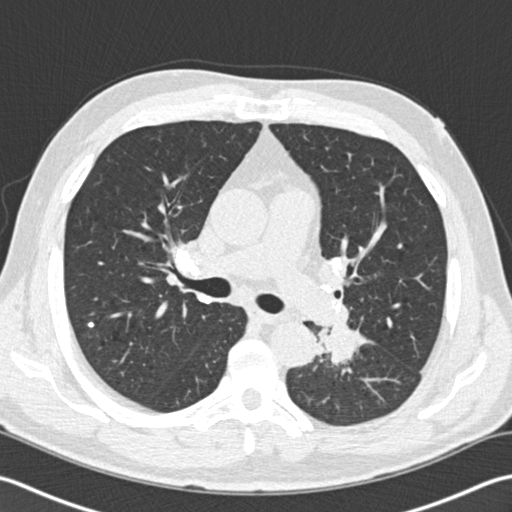
Low-dose screening chest CT, one axial slice; slice 107 of 170 in the series (ordered by position); reconstruction kernel B30f; lung window (W 1500 / L -600 HU); 512 × 512 image matrix, field of view 350 × 350 mm.
Structures marked on this image (expert manual segmentation):
- lesion 1 (tumor, lower lobe of left lung): bounding box (x1, y1, x2, y2) in pixels: (318, 322, 368, 363)